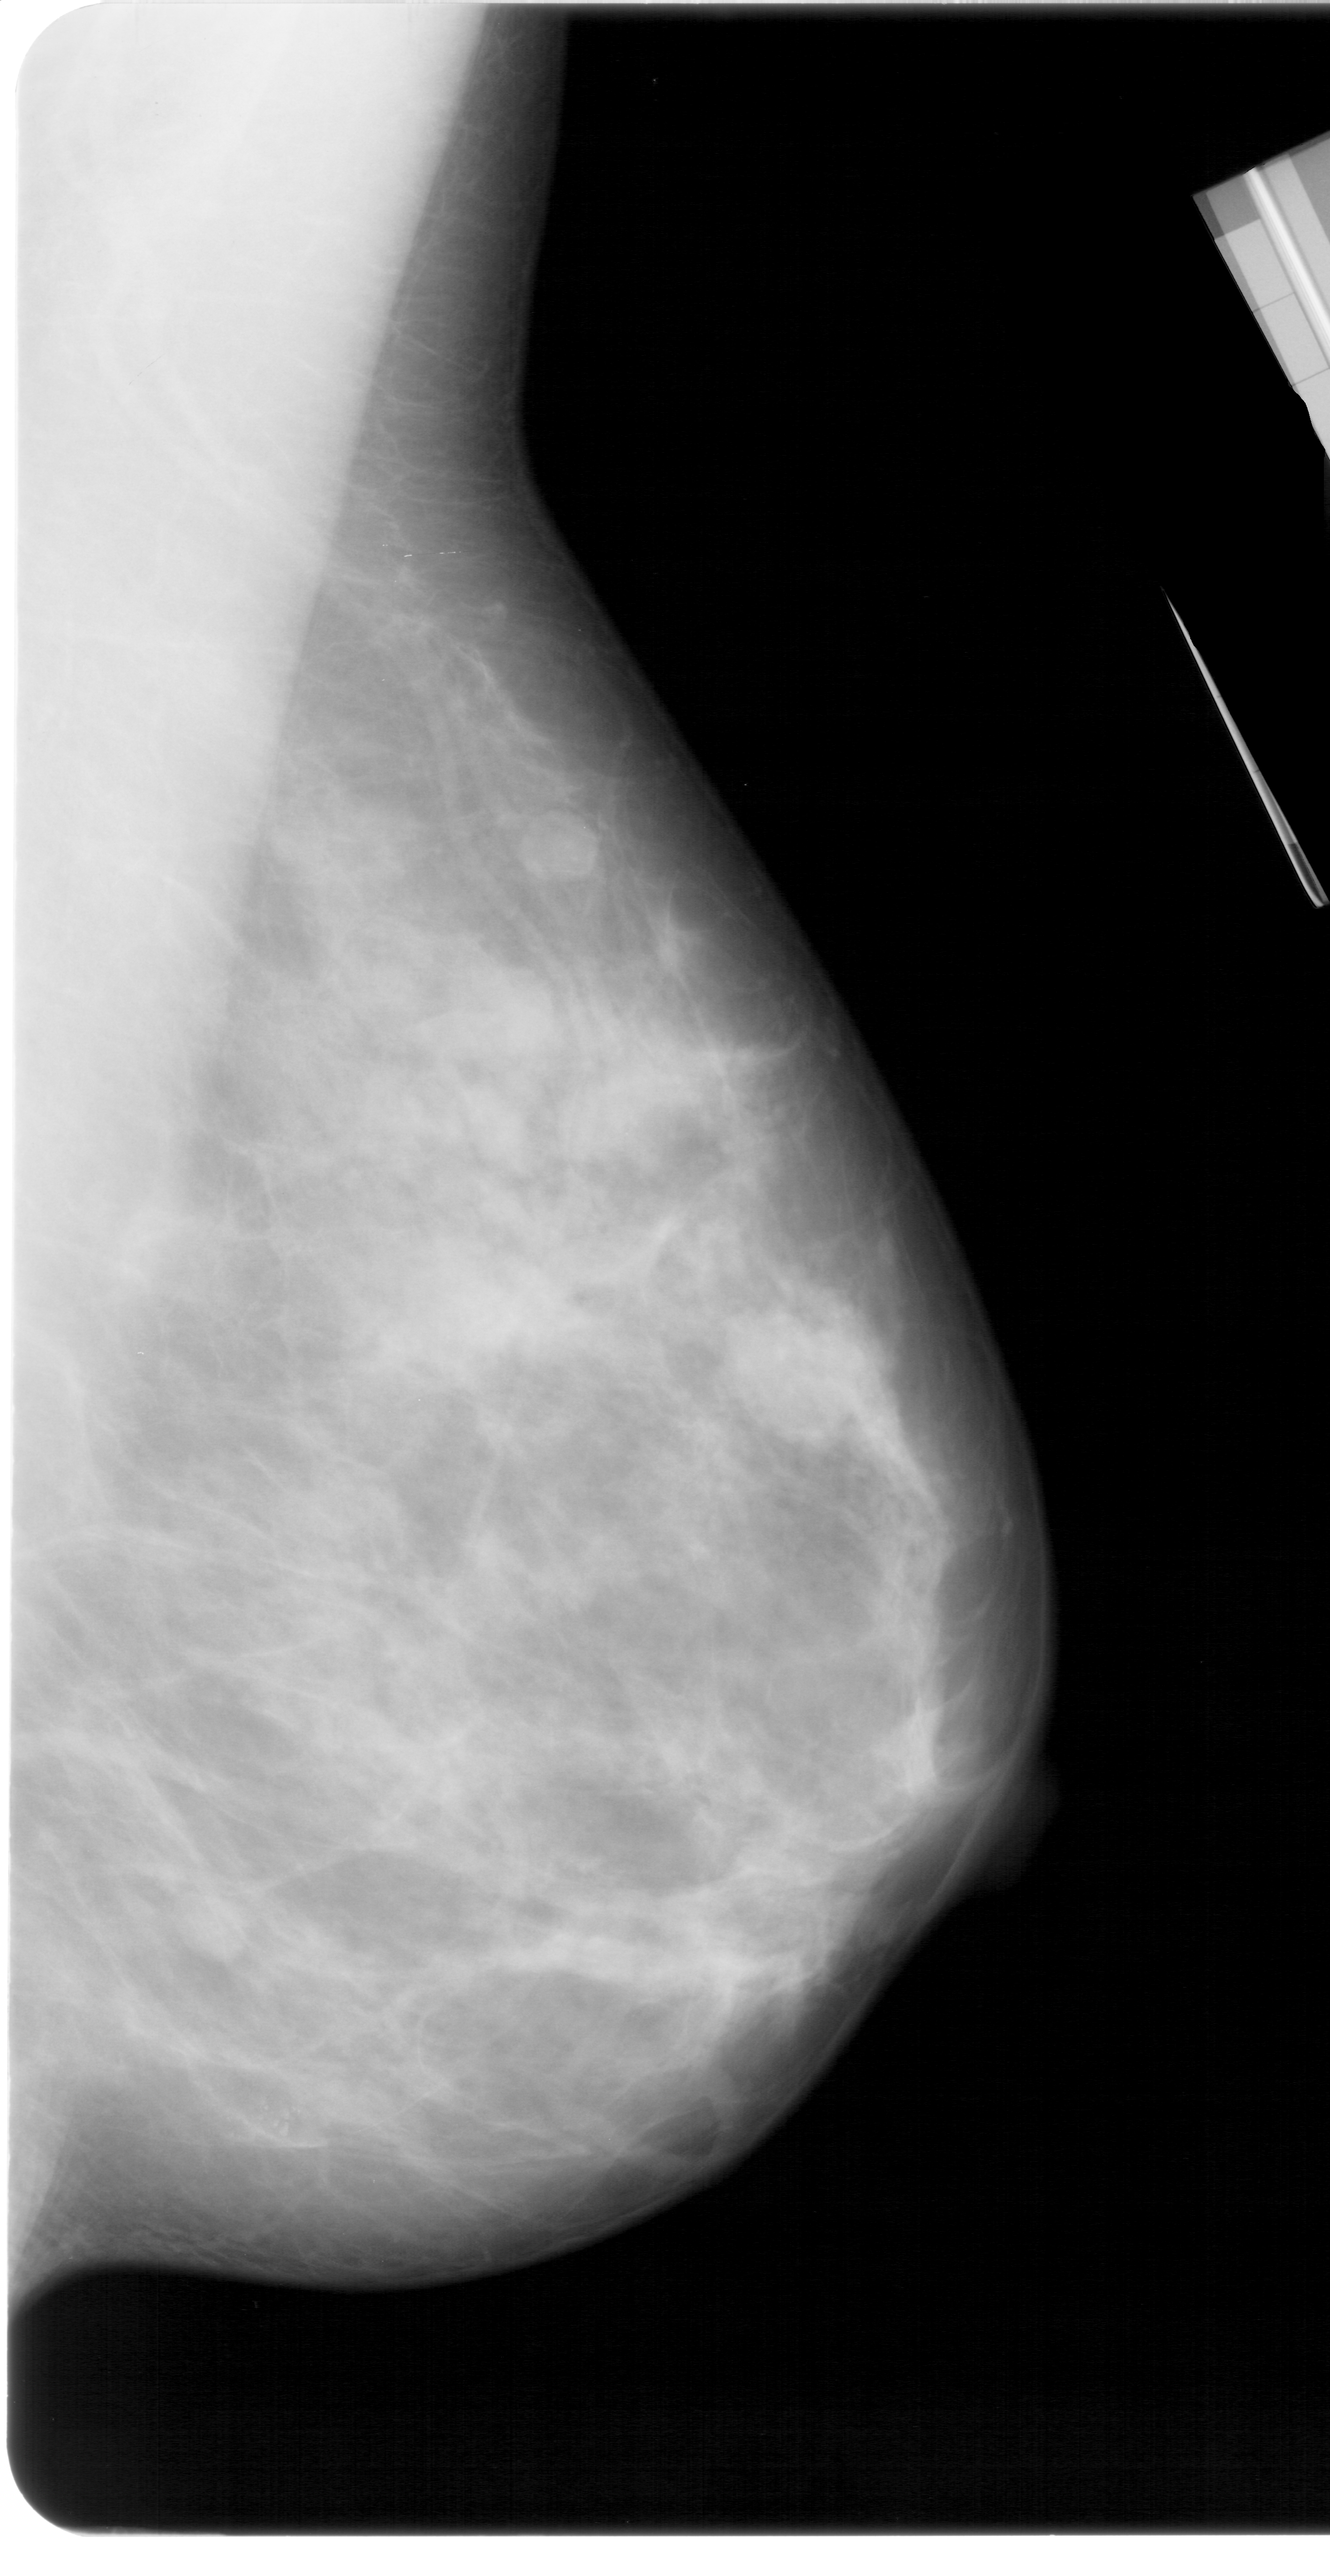
Digitized screen-film mammogram; right breast; MLO view; breast composition: extremely dense (BI-RADS density category 4 of 4); 1330 × 2576 image matrix.
Expert-marked regions of interest on this image (one box per marked abnormality):
- calcifications, morphology pleomorphic, distribution clustered; BI-RADS assessment category 4; subtlety rating 2 on a 1 (subtle) to 5 (obvious) scale; pathology (as recorded): malignant: bounding box <170,2069,322,2176> (left, top, right, bottom; pixels)